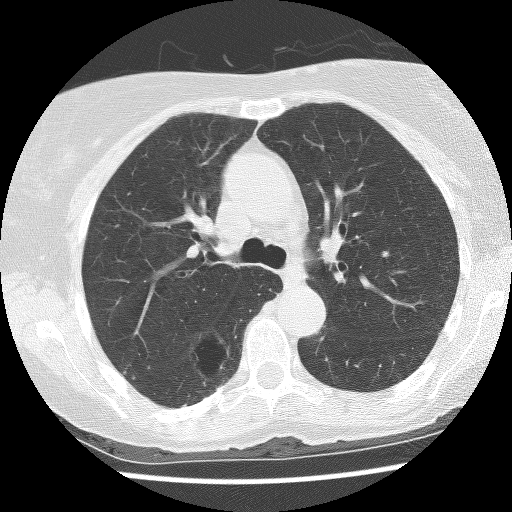
Chest CT (low-dose screening protocol), one axial image; baseline annual screen; lung window (W 1500 / L -600 HU); 2.5 mm slice thickness; lung (sharp) reconstruction kernel (BONE); 120 kVp; slice 42 of 136 in the series. Female participant, aged 69 years at enrolment. Former smoker at enrolment.
Lesion marked by an expert reader, bounding box (x1, y1, x2, y2) in pixels: (171, 323, 244, 396). The screening reader recorded 2 non-calcified nodules or masses ≥4 mm on this exam (right lower lobe, right lower lobe); which of them this box marks is not recorded. Later outcome: lung cancer diagnosed 288 days after this screen — non-small cell carcinoma, right lower lobe, poorly differentiated (G3), stage IB (AJCC 6th edition), 36 mm at pathology.